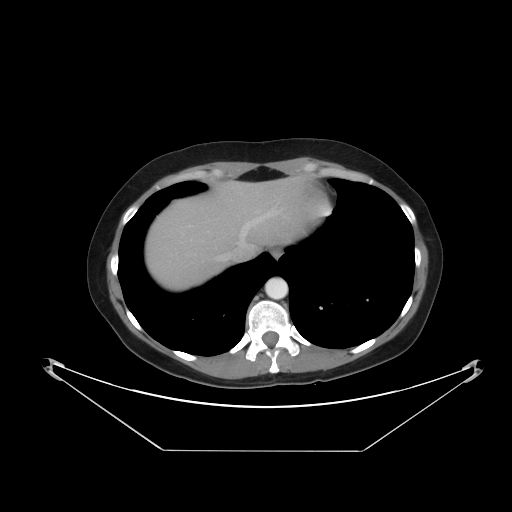
Contrast-enhanced abdominal CT, one axial slice. Reconstruction kernel STANDARD. 120 kVp. Intravenous contrast given. Soft-tissue window (W 400 / L 40 HU). 5 mm slice thickness. 512 × 512 image matrix, field of view 482 × 482 mm. Female patient, age 38 years. Case-level facts recorded for this patient, not image findings: diagnosis: colorectal cancer liver metastases, imaged before liver resection; multiple liver metastases: yes; largest metastasis: 2.5 cm; chemotherapy before resection: no.
Annotated regions visible in this slice (expert manual segmentation):
- hepatic veins: bounding box (x1, y1, x2, y2) in pixels: (220, 208, 278, 259)
- liver: (146, 180, 307, 291)
- planned liver remnant (the part of the liver to remain after resection): (210, 180, 307, 248)